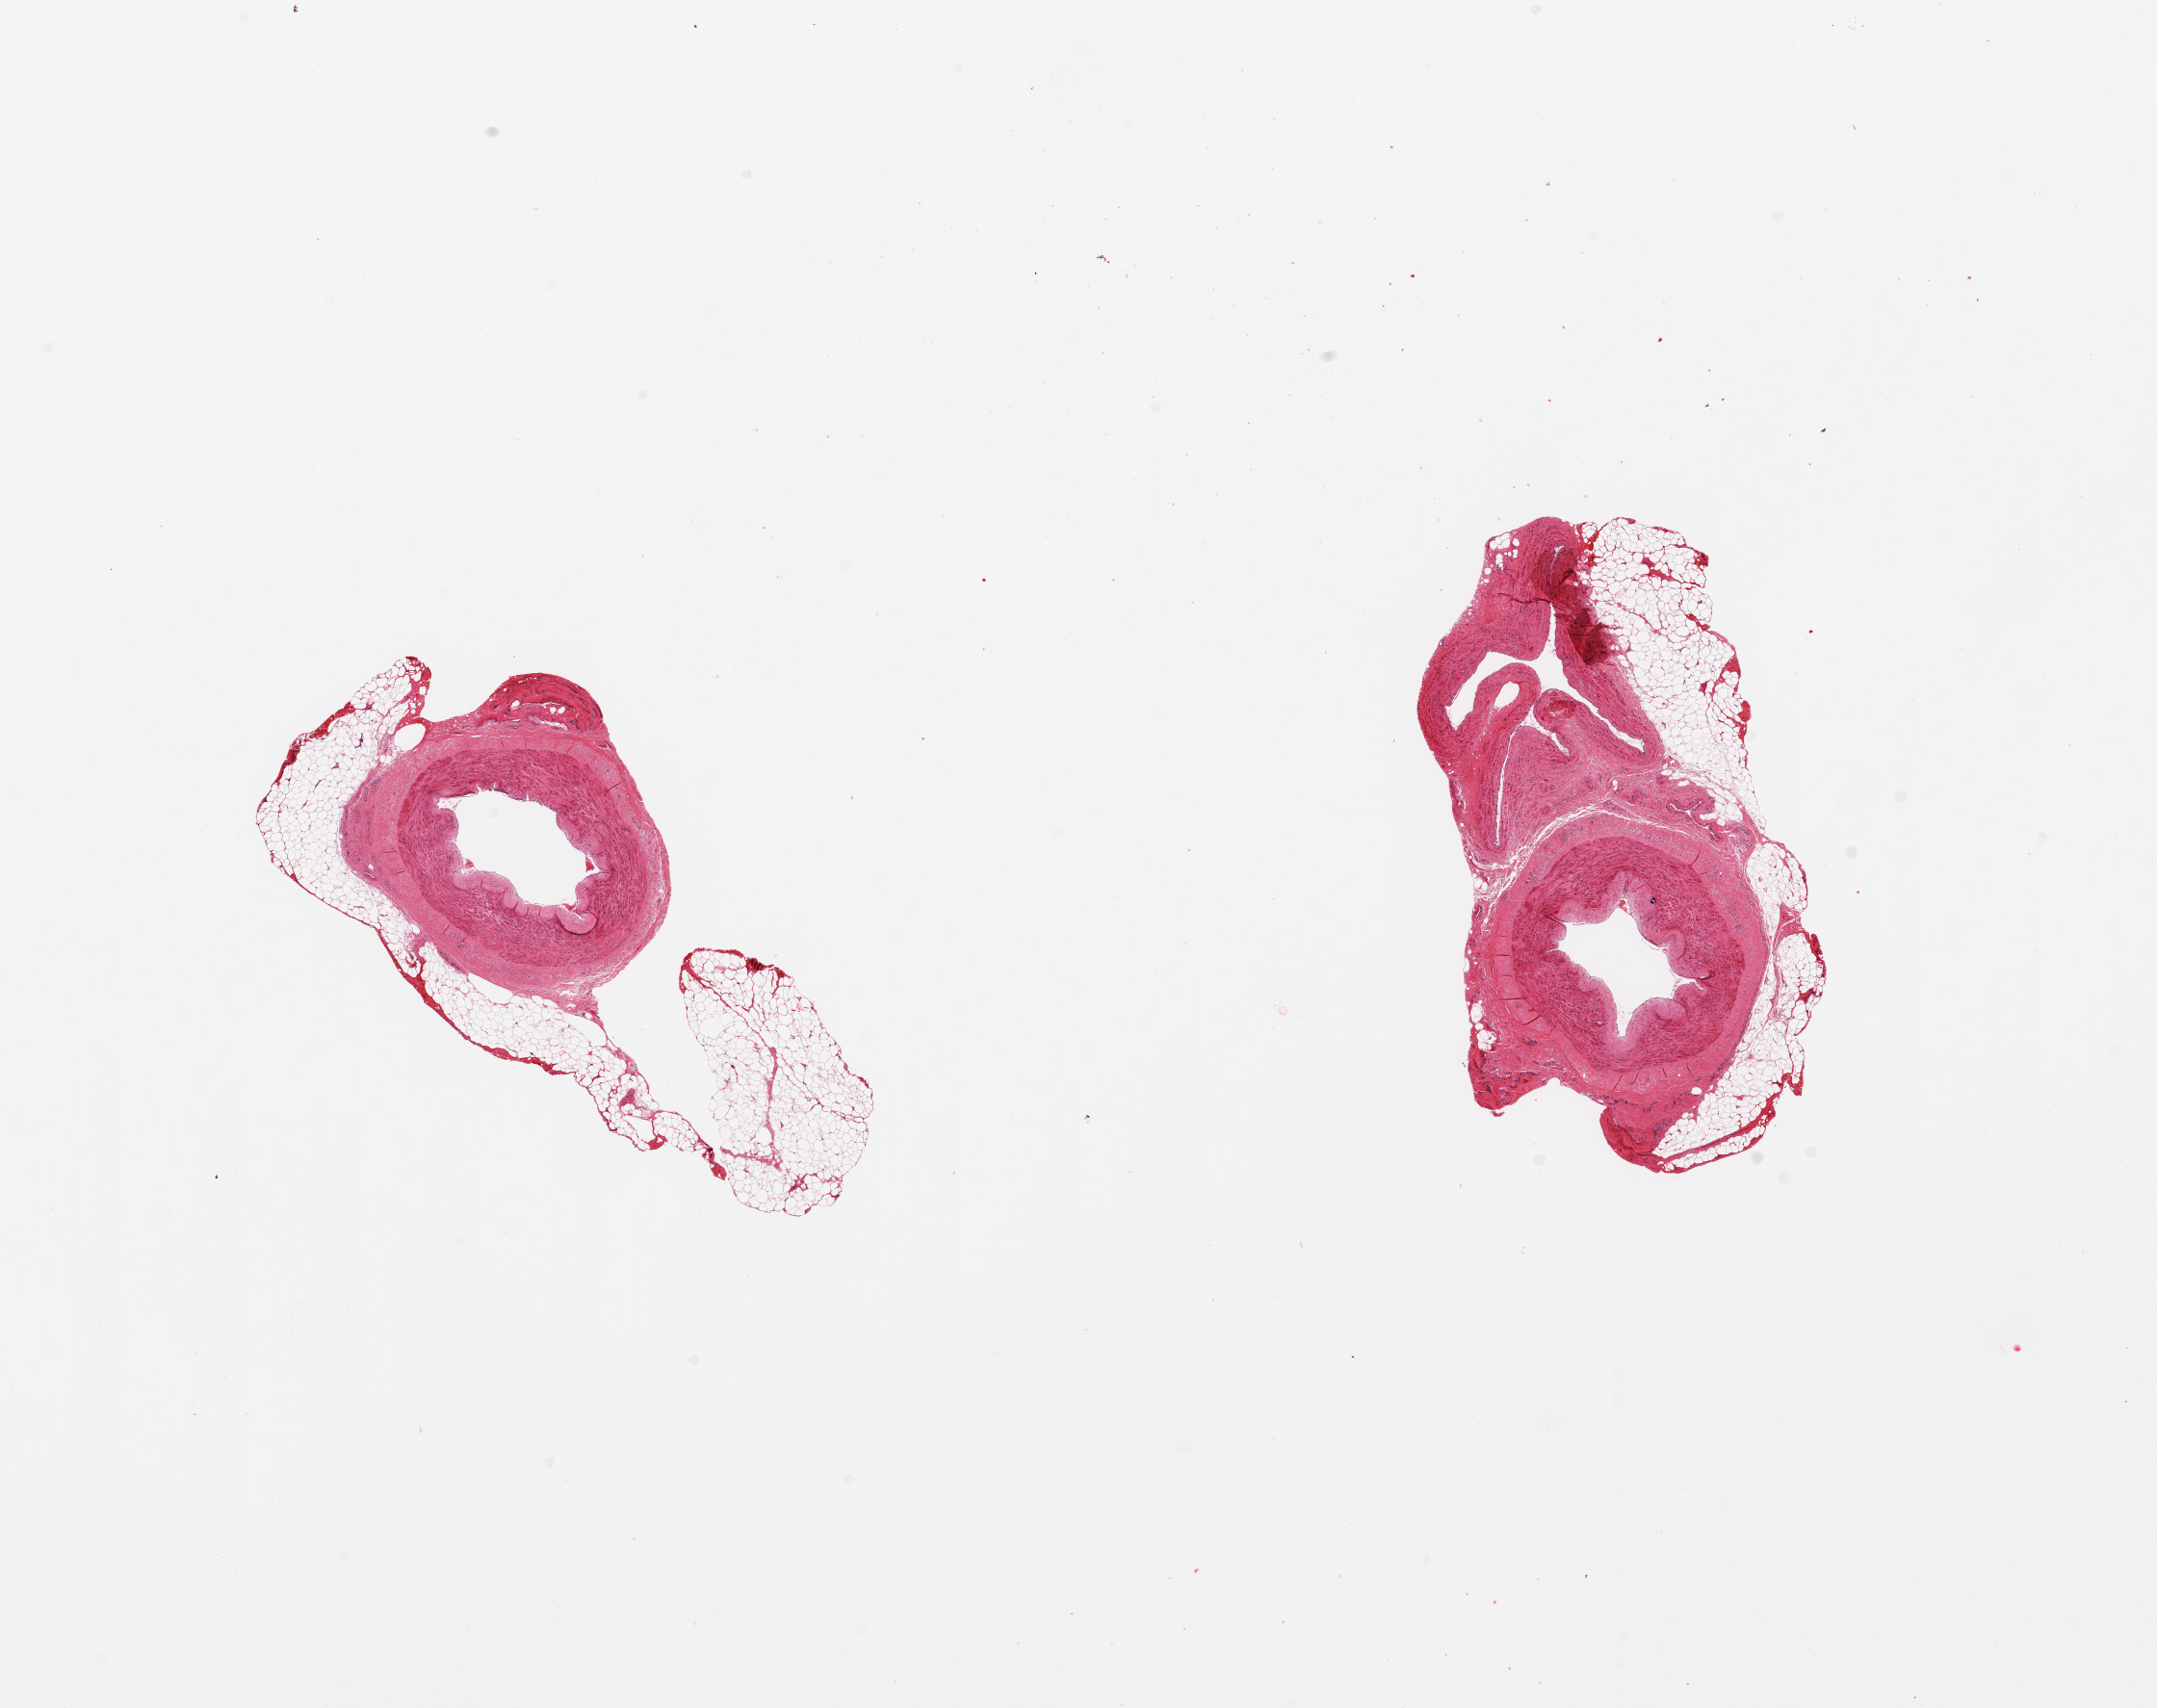
Hematoxylin and eosin (H&E) whole-slide image, brightfield — low-resolution overview of the scanned area, about 17.7 x 14.0 mm; PAXgene-fixed paraffin-embedded (PFPE) section; sampled site (target tissue): tibial artery; donor tissue sample. Donor sex: male.
• reviewer comment on this tissue sample: 2 pieces, adherent nubbins of fat up to ~1mm, adherent vein in one section